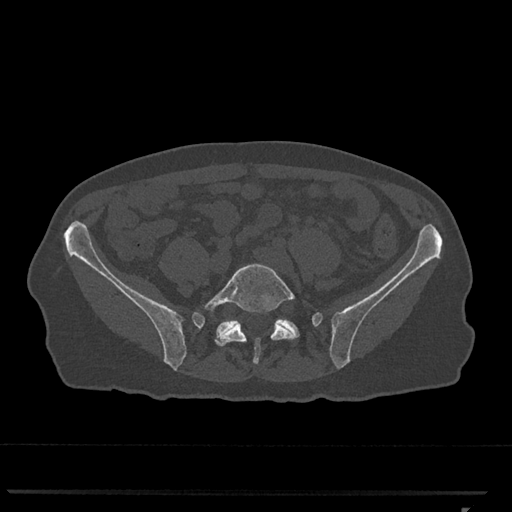
CT including the spine, one axial slice; slice 139 of 793 in the series (ordered by position); reconstruction kernel Br40s/3; 120 kVp; bone window (W 1800 / L 400 HU); 0.5 mm slice thickness; 512 × 512 image matrix. Patient: female, 62 years. Case-level facts recorded for this patient, not image findings: primary cancer: renal.
Outlined on this slice (semi-automatically segmented with operator editing):
- L5 vertebra: box from (x=204, y=263) to (x=296, y=365) px